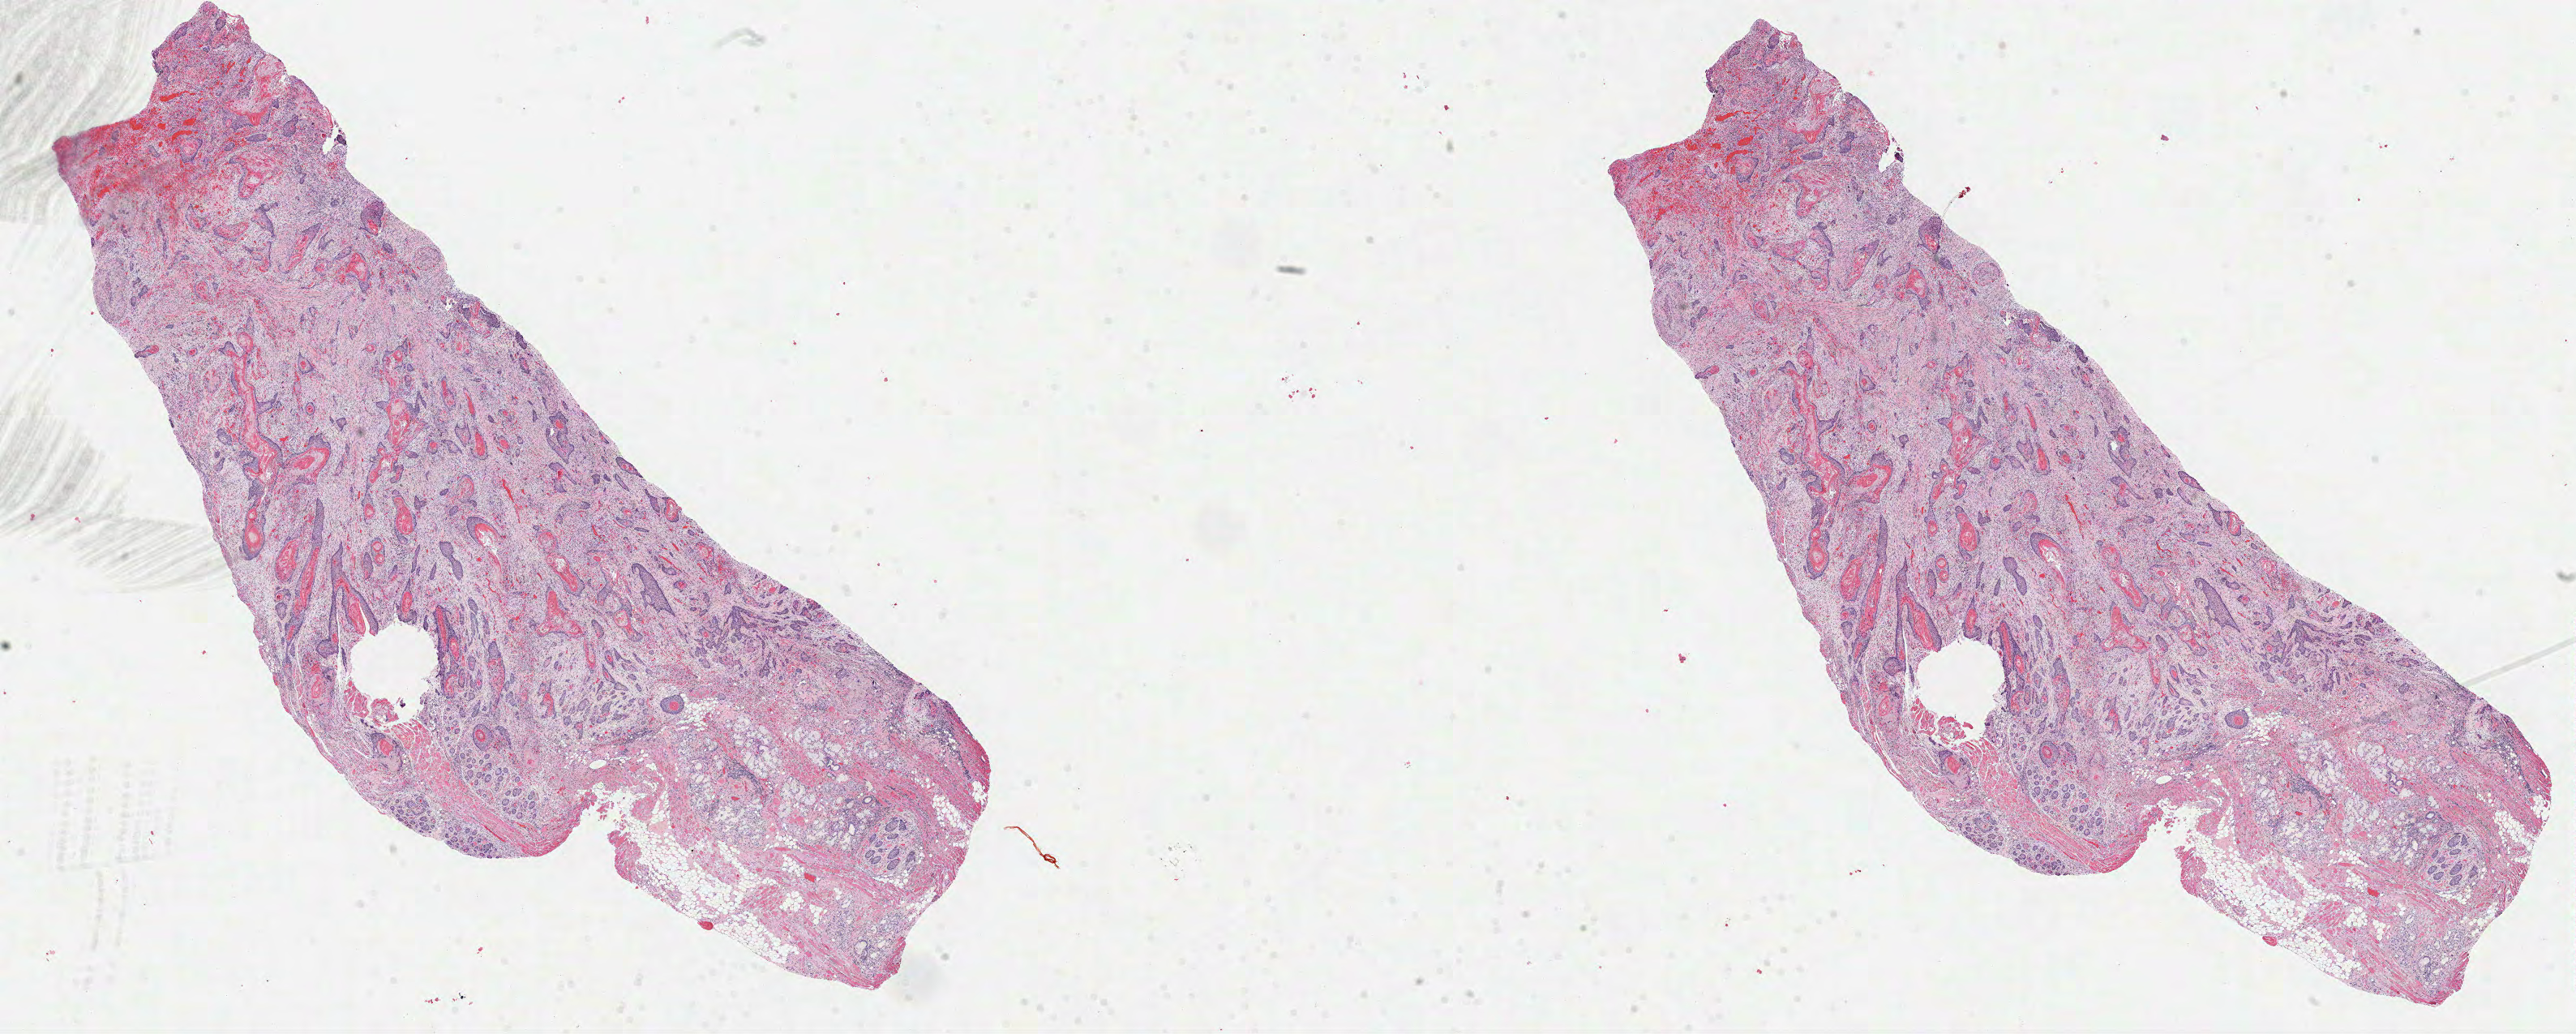
Whole-slide histology image, H&E — shown as a low-resolution overview of the whole scanned area (about 25.6 x 10.3 mm); formalin-fixed paraffin-embedded (FFPE) diagnostic section; sample: primary tumour, head and neck. Male patient; age at initial diagnosis 61 years. Histologic grade: G2 (moderately differentiated).
AJCC pathologic stage: IVA. Diagnosis: Squamous cell carcinoma, NOS (tongue, NOS).